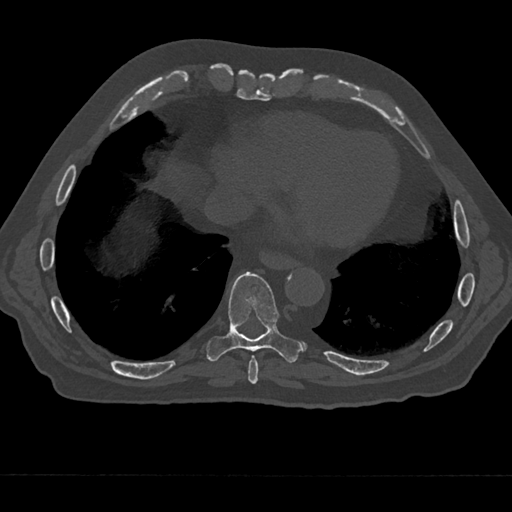
CT including the spine, one axial slice. Position 267 of 797 along the scan axis. Reconstruction kernel Br40s/3. 120 kVp. Bone window (W 1800 / L 400 HU). 0.5 mm slice thickness. 512 × 512 image matrix, field of view 377 × 377 mm. Male patient, age 75 years. Case-level facts recorded for this patient, not image findings: primary cancer: renal.
Structures marked on this image (semi-automatically segmented with operator editing):
- T8 vertebra: box from (x=248, y=355) to (x=259, y=384) px
- T9 vertebra: (x=206, y=272)–(x=302, y=363)